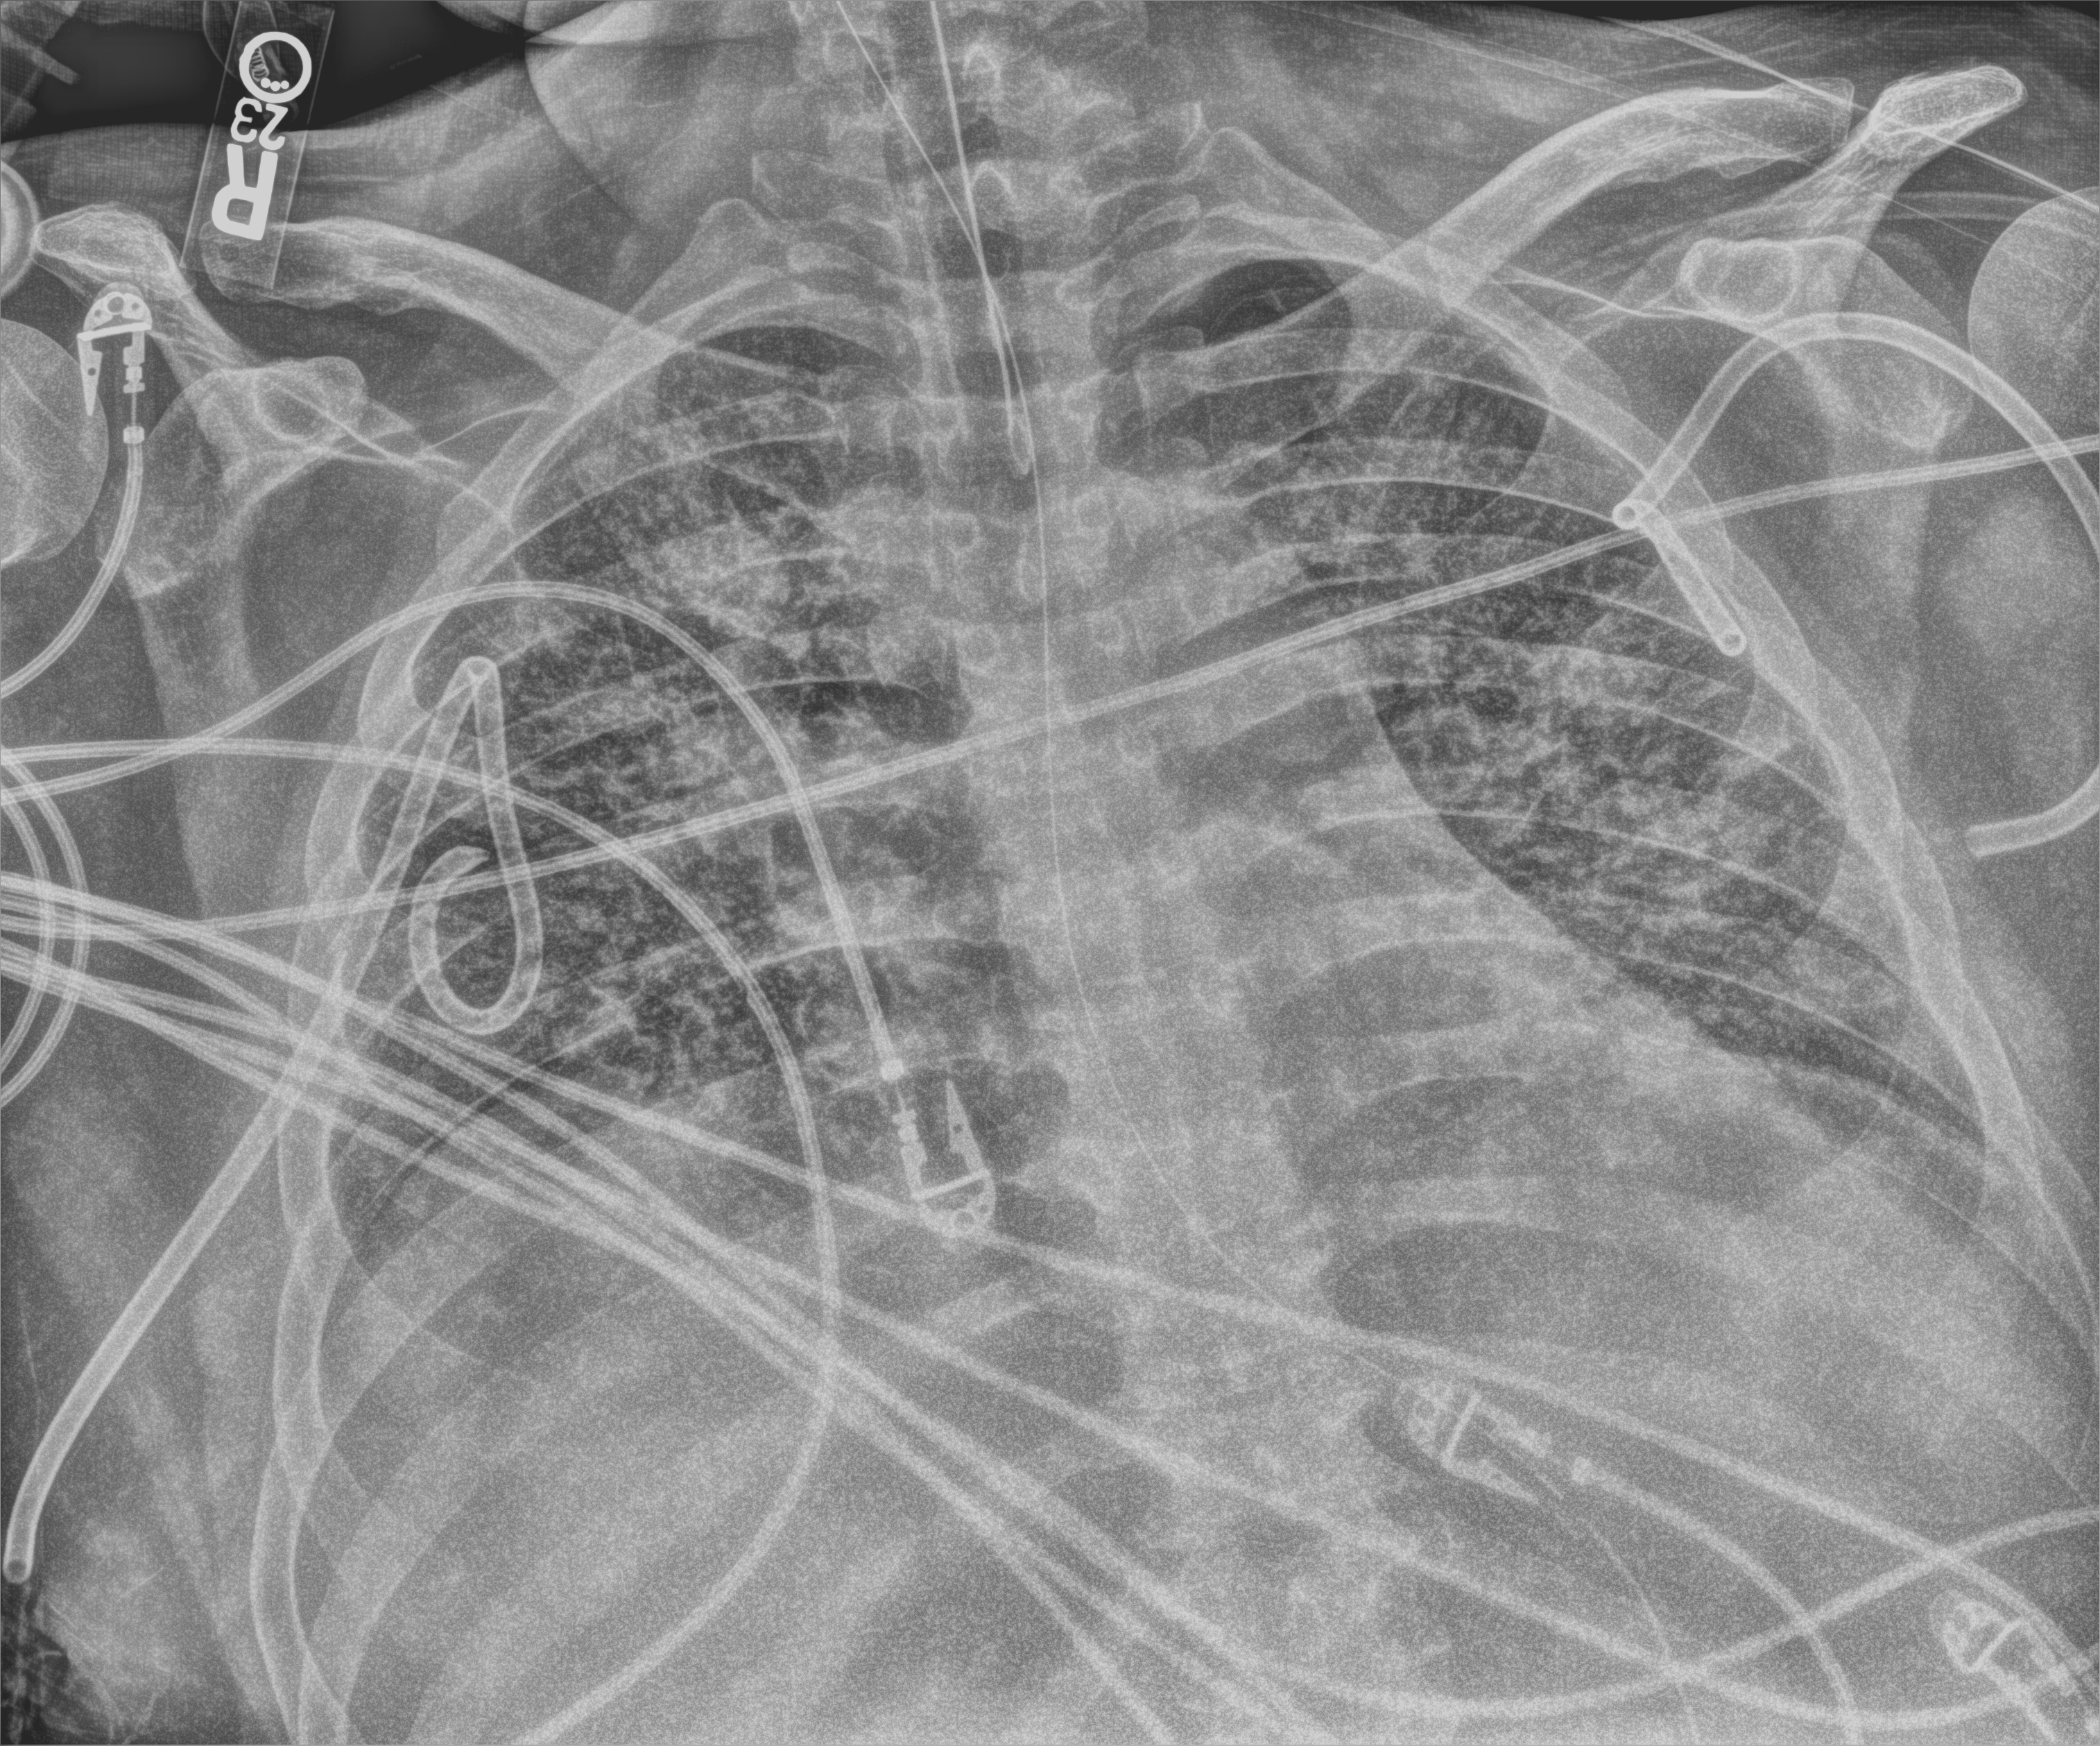
Bedside chest radiograph (computed radiography); anteroposterior (AP) projection. Patient hospitalised with COVID-19, aged 18–59 years.
Admission-level facts for this patient (not findings on this image; timing relative to this image not recorded): mechanically ventilated during this hospital stay: yes.